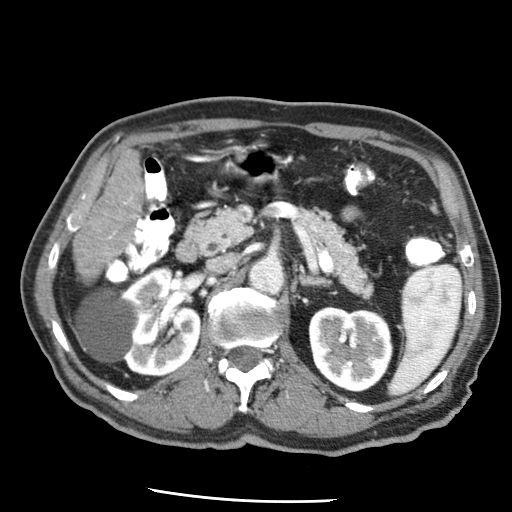
Contrast-enhanced abdominal CT (liver protocol), one axial slice; position 15 of 79 along the scan axis; soft-tissue window (W 400 / L 40 HU); 2.5 mm slice thickness; 512 × 512 image matrix. Case-level facts recorded for this patient, not image findings: diagnosis: hepatocellular carcinoma (patient treated with transarterial chemoembolisation; whether this scan precedes or follows treatment is not stated here); TNM stage (as recorded): Stage-IIIA; Child-Pugh class: A; tumour differentiation: moderately differentiated; tumour nodularity: multinodular.
Structures marked on this image (semi-automatic segmentation, software-assisted and operator-edited):
- liver parenchyma outside the tumour (the mass and vessels are separate outlines, so this box may not span the whole liver): box from (x=96, y=150) to (x=142, y=236) px
- liver vessels: (x=124, y=196)–(x=133, y=204)